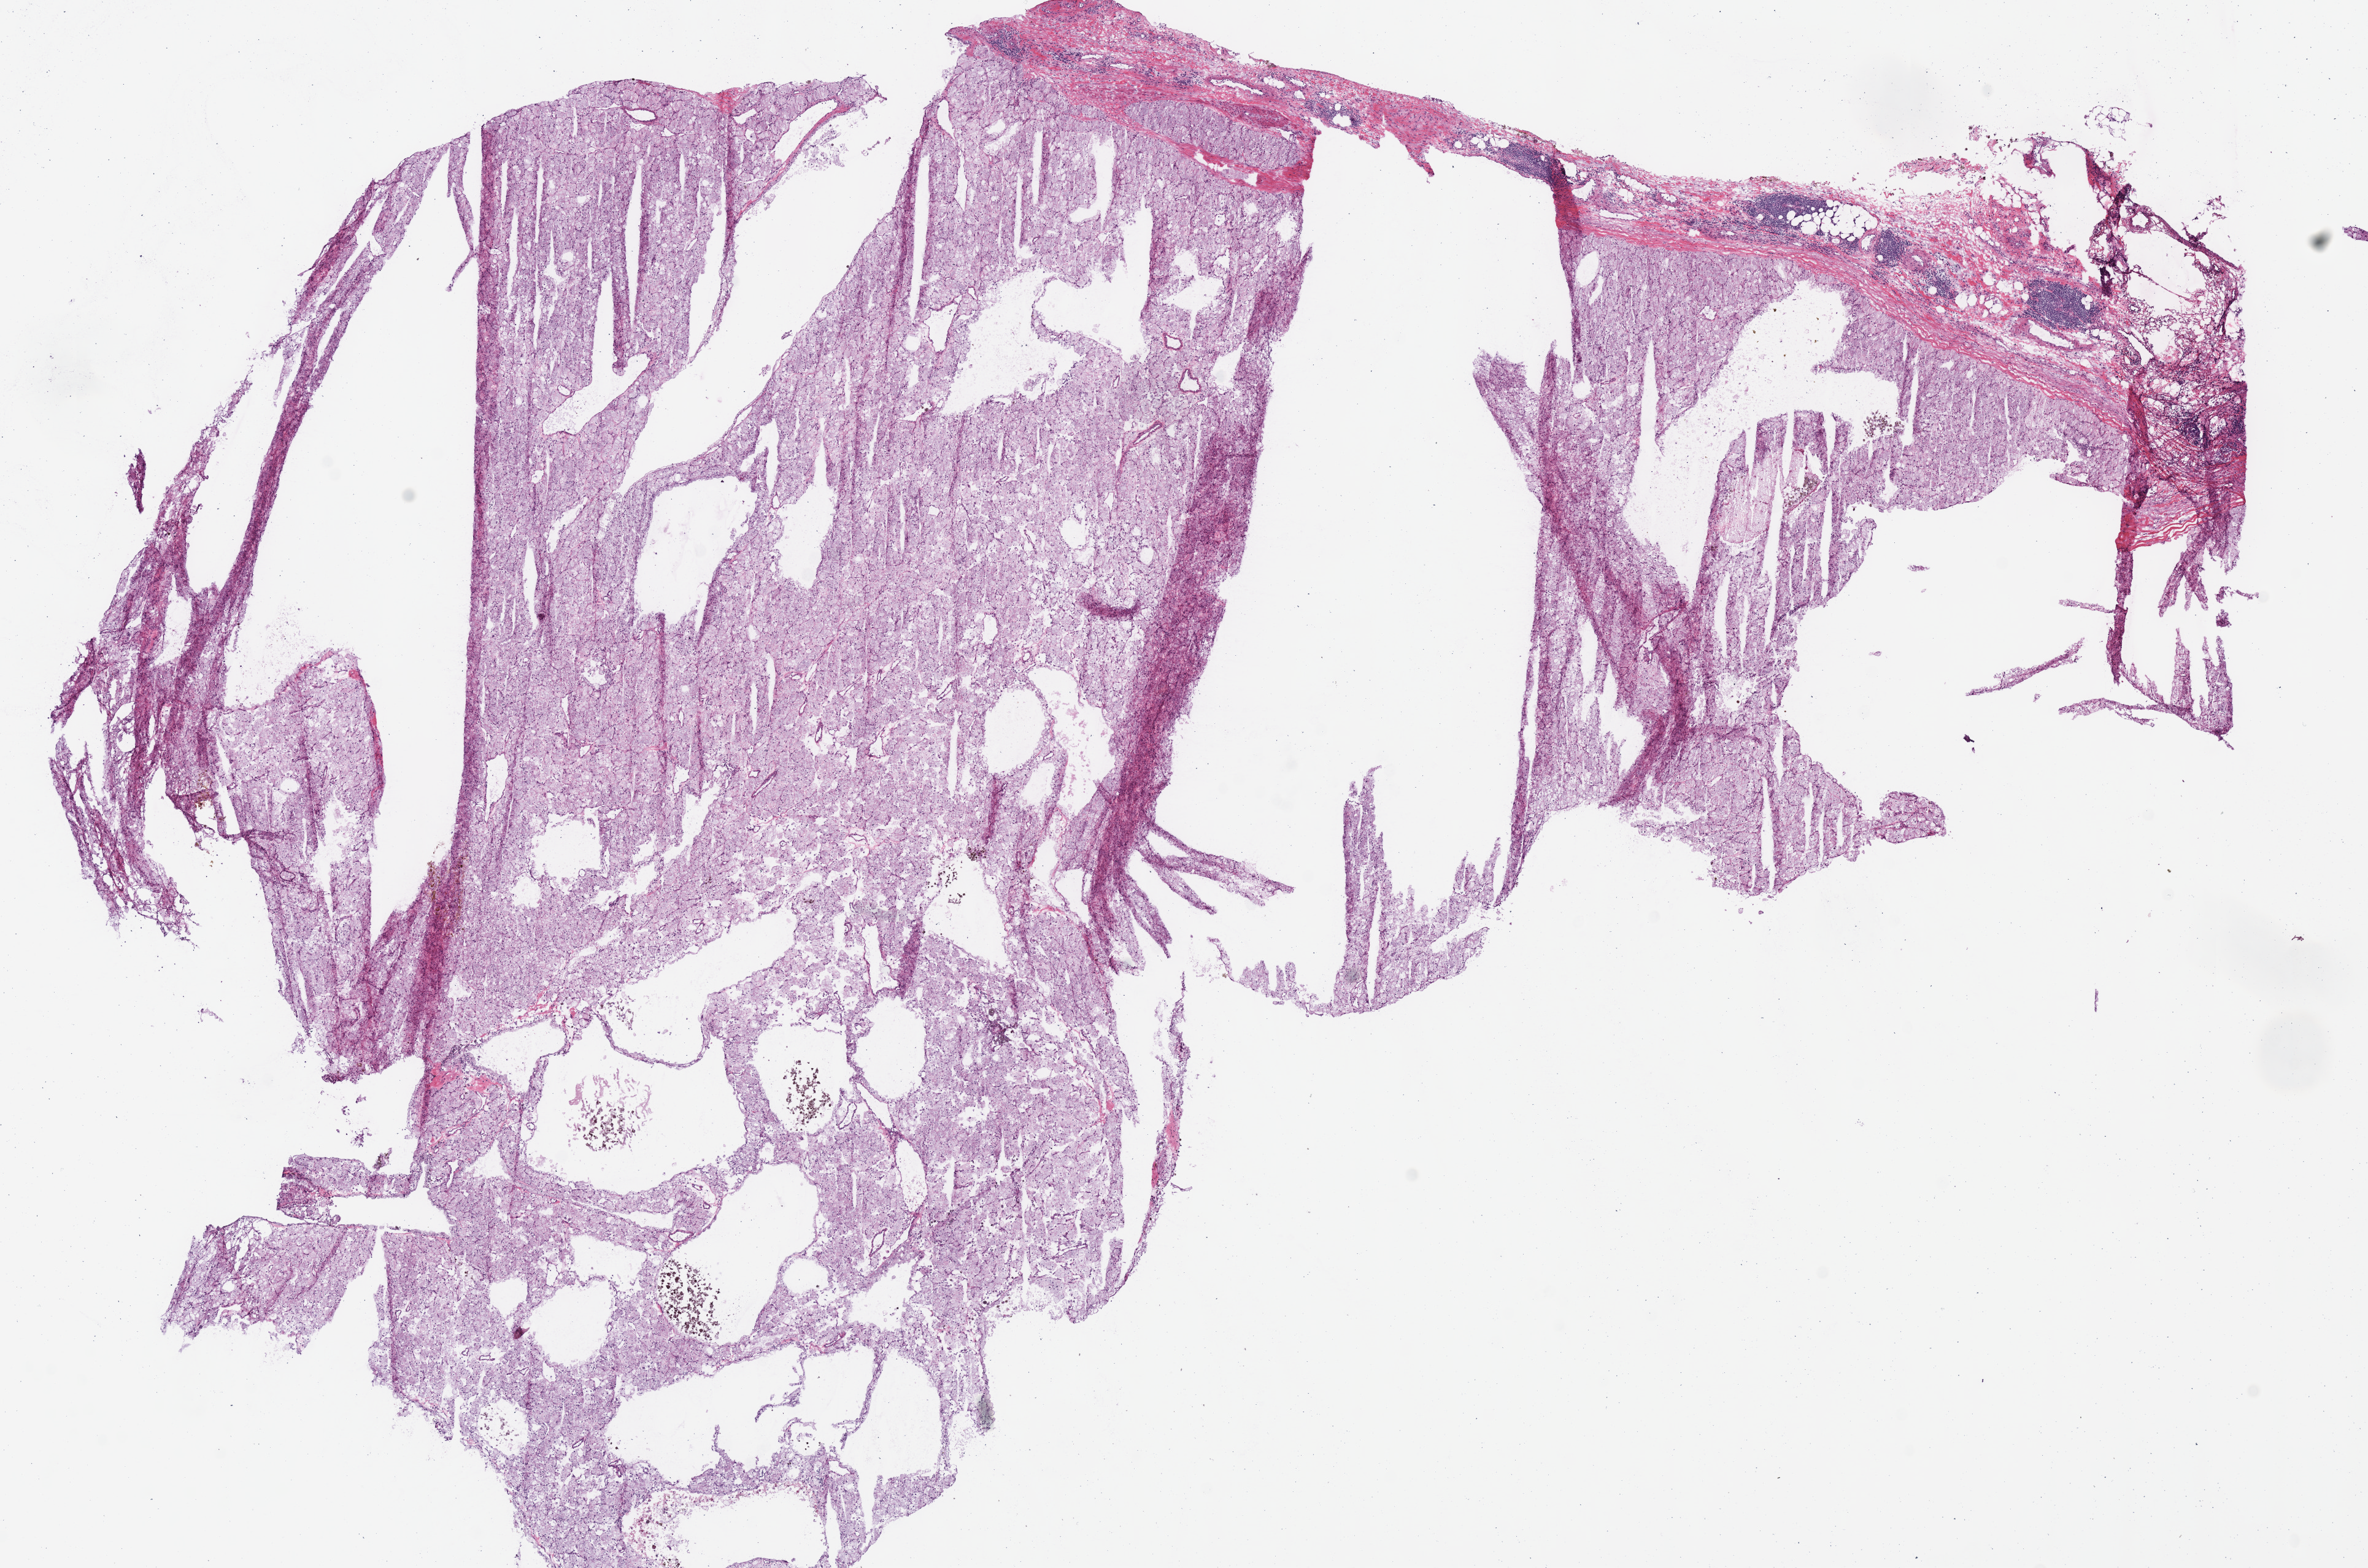
Whole-slide histology image, H&E-stained — low-resolution overview of the scanned area, about 15.2 x 10.0 mm (from a 40x scan). Frozen section. Primary tumour sample from the kidney. Patient: male, age at initial diagnosis 69 years. Slide review estimates, as recorded: tumour cells 90%, tumour nuclei 85%, normal cells 0%, stromal cells 10%, necrosis 0%. Inflammatory infiltration, as recorded: lymphocyte infiltration 5%, monocyte infiltration 5%, neutrophil infiltration 0%.
TNM: T2 N0 M0. Pathologic diagnosis: Renal cell carcinoma, chromophobe type. Lymph nodes positive (case pathology): 0 of 5 examined. Laterality: left. AJCC pathologic stage: II (6th edition).